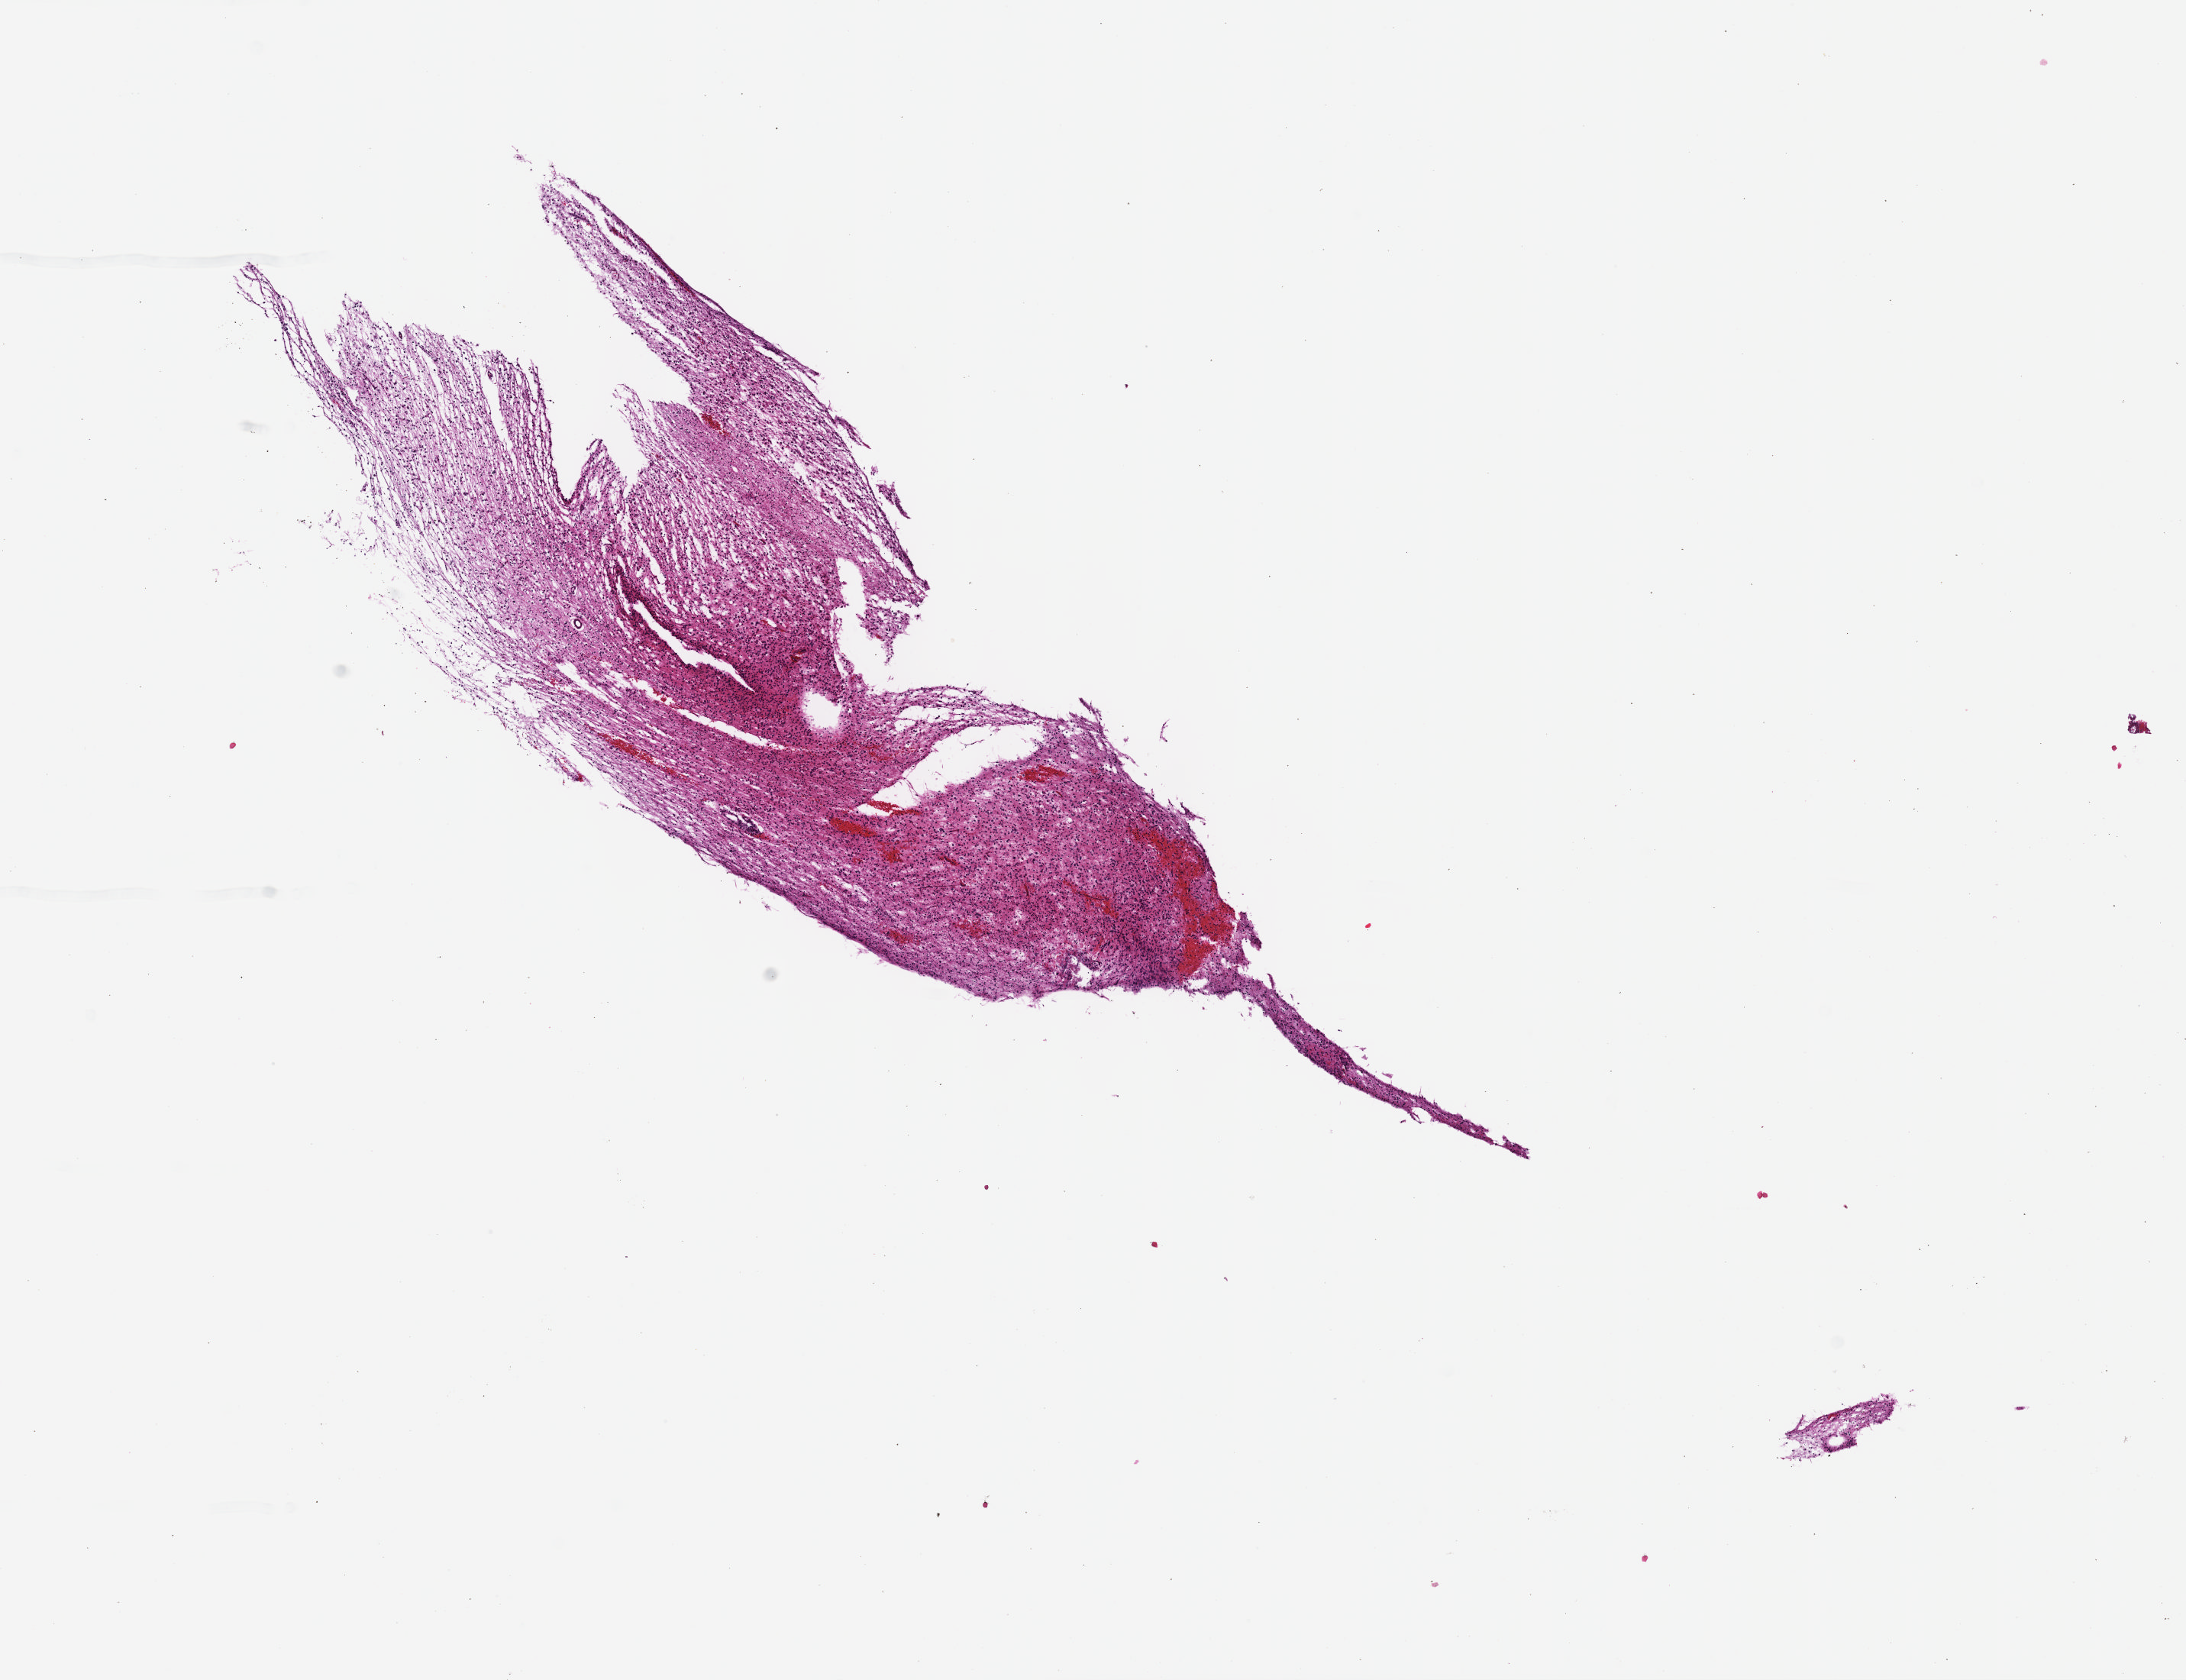
Digitized H&E-stained tissue section (whole slide) — shown as a low-resolution overview of the whole scanned area (about 11.6 x 8.9 mm). FFPE section. Sample: primary tumour, brain. Patient: male, age at initial diagnosis 24 years. Histologic grade: G2 (moderately differentiated).
• laterality: right
• histologic diagnosis: Astrocytoma, NOS (cerebrum)